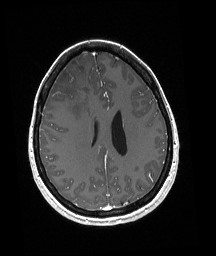
Brain MRI from a brain-tumour surgery series, one axial slice. Slice 75 of 192 in the series (ordered by position). T1-weighted post-contrast. 1 mm slice thickness. 216 × 256 image matrix. From the clinical record (not read from this slice): histopathology: Oligodendroglioma; WHO grade: 3; IDH mutation: yes; tumour location: Right Frontal.
Outlined on this slice (outlined manually by an expert reader):
- tumour: bounding box <62,83,87,91> (left, top, right, bottom; pixels)